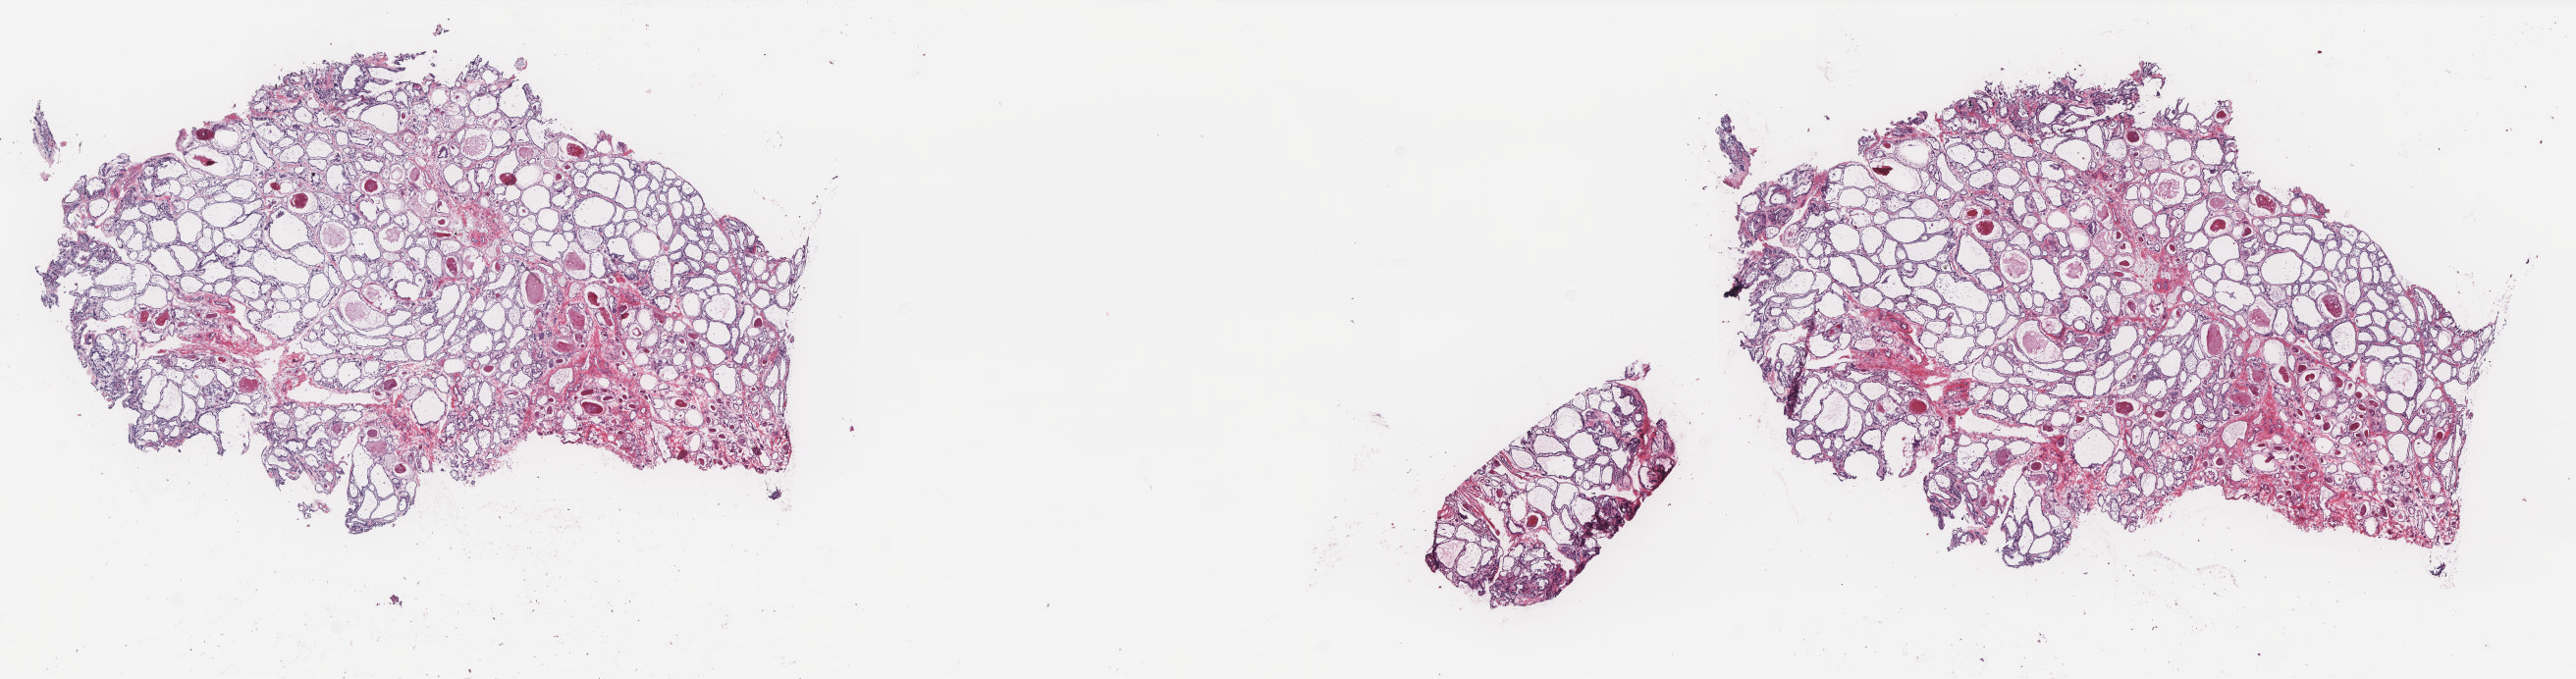
H&E-stained whole-slide image — low-resolution overview of the scanned area, about 21.0 x 5.5 mm. Frozen section from the top of the tissue portion. Sample: solid tissue normal (non-tumour tissue), thyroid. Female patient; age at initial diagnosis 43 years.
This section: solid tissue normal (non-tumour) sample from the same patient. Patient diagnosis: Papillary adenocarcinoma, NOS (thyroid gland).